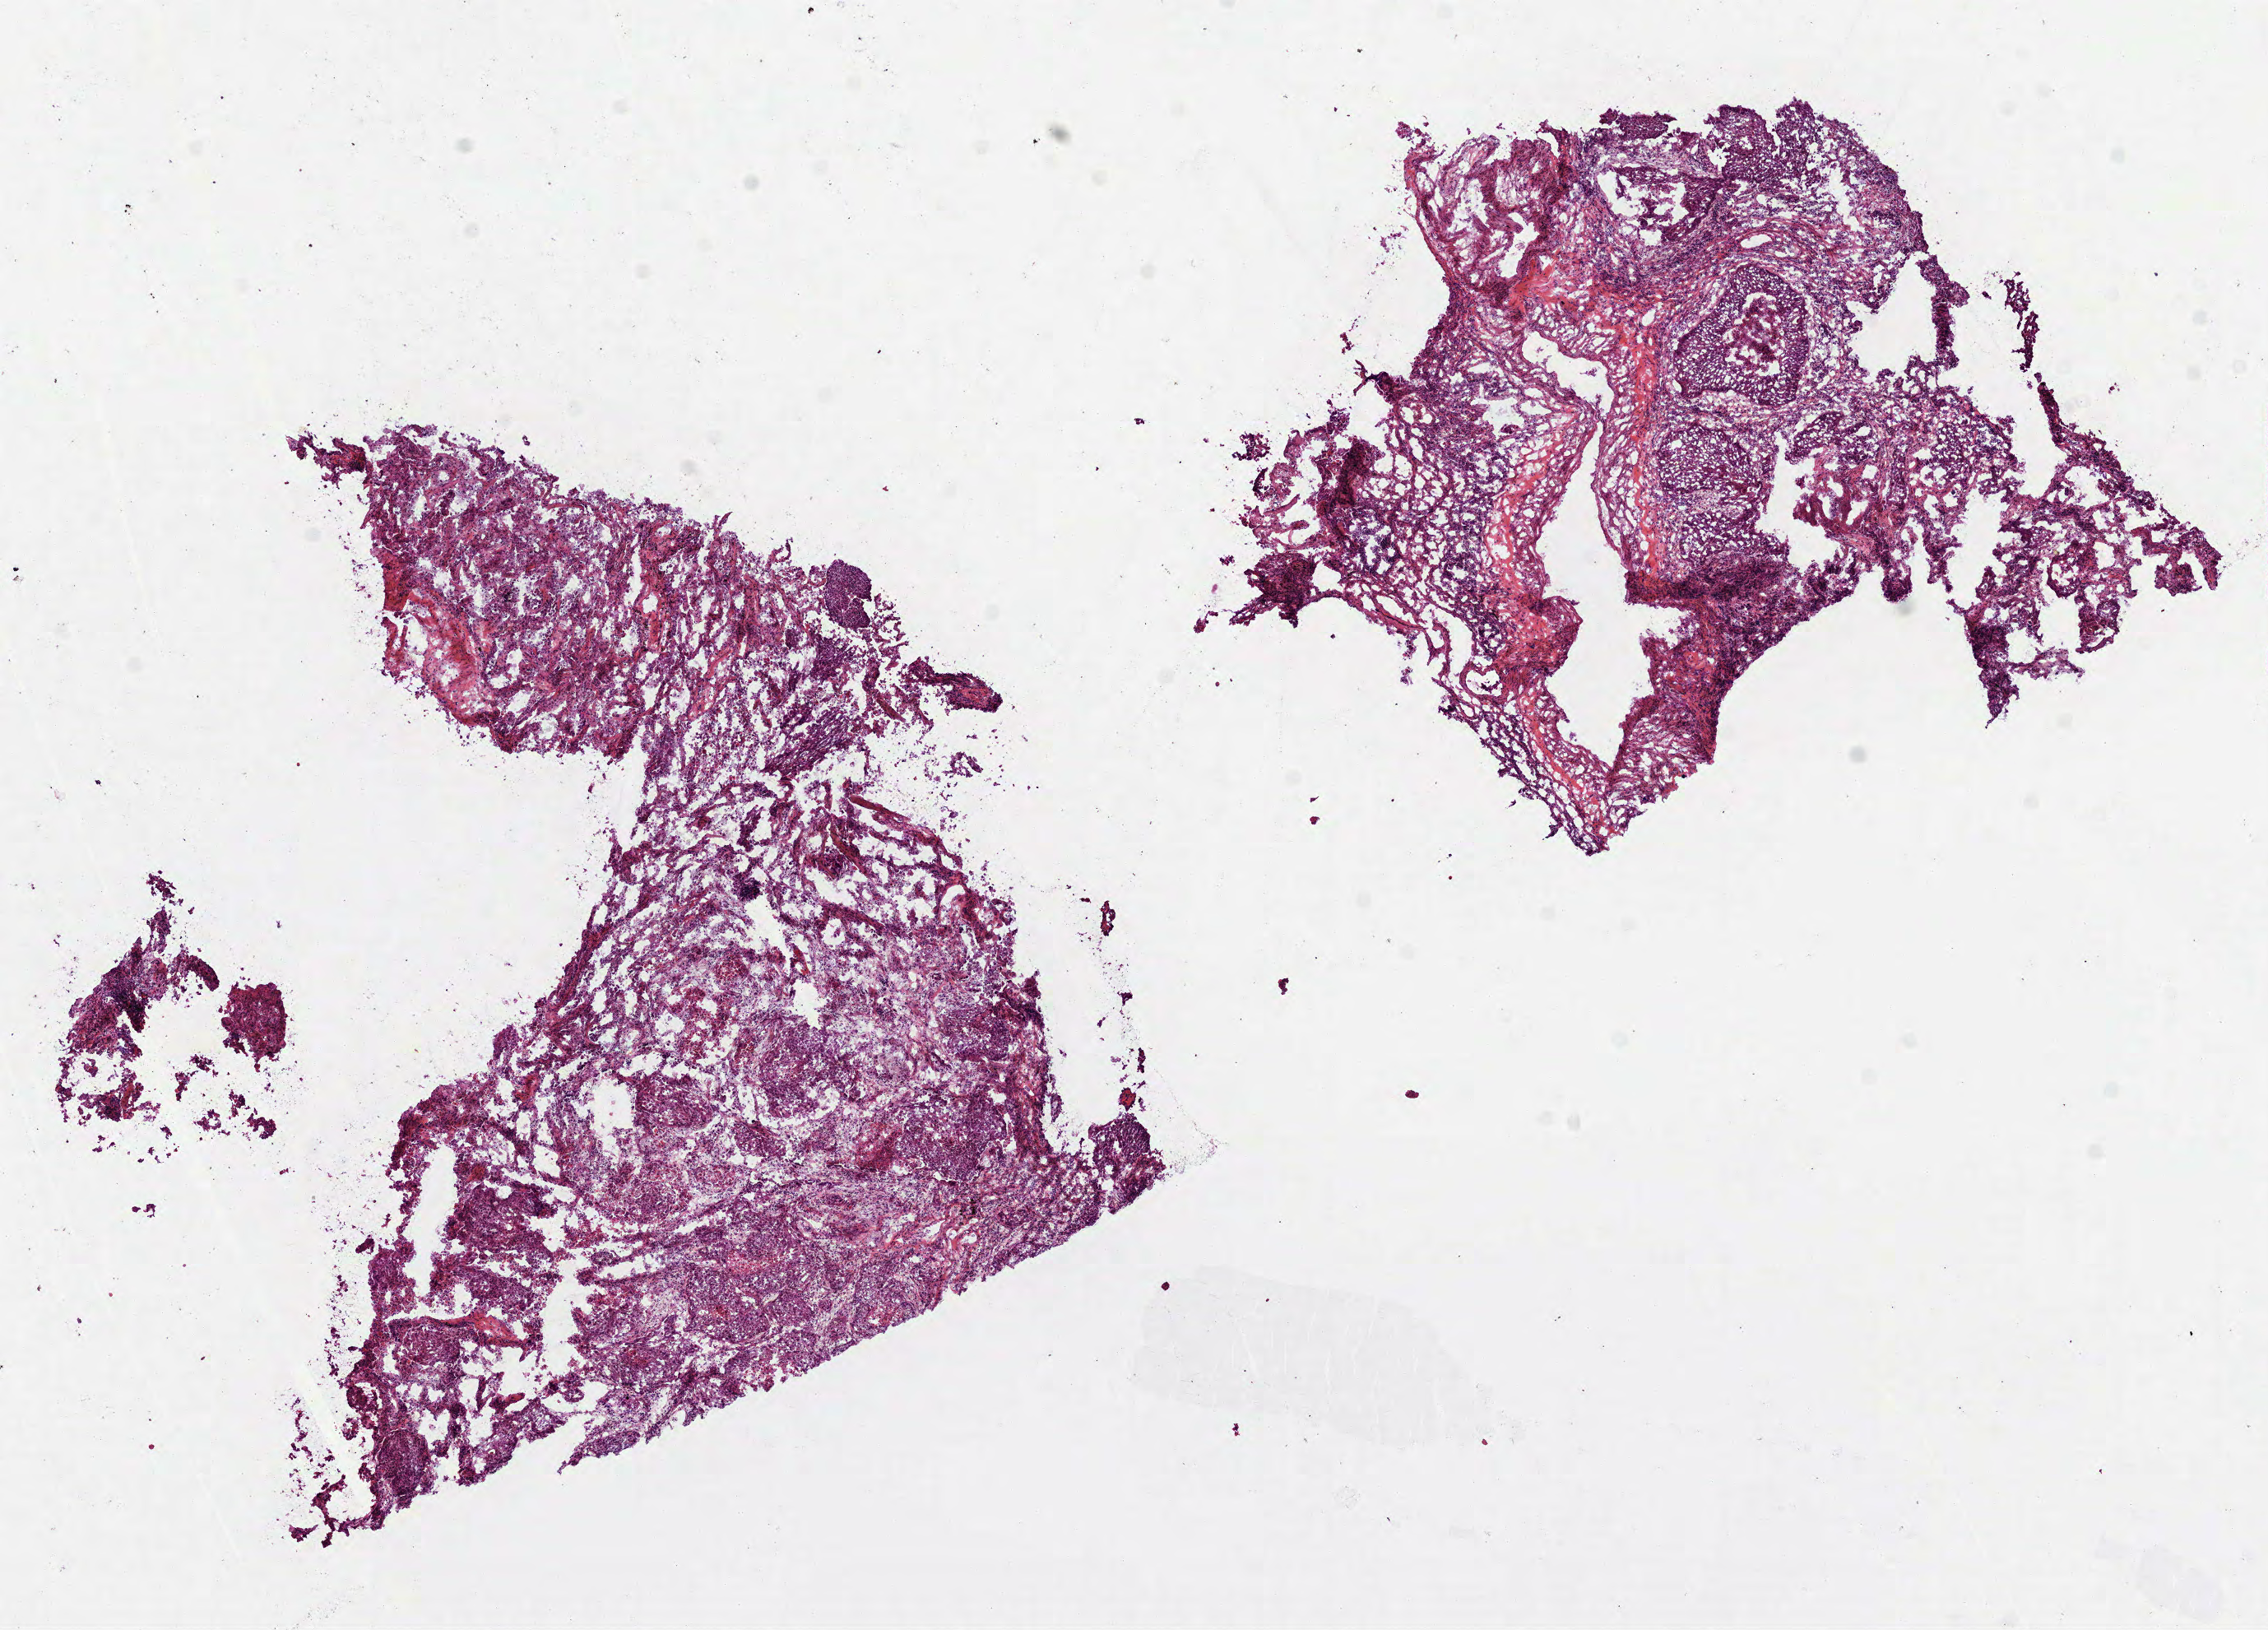
Hematoxylin and eosin (H&E) stained whole-slide image — a low-resolution overview of the entire scanned area, about 11.1 x 8.0 mm (slide scanned at 40x); frozen section from the bottom of the tissue portion; primary tumour sample from the lung. Patient: male, age at initial diagnosis 73 years. Composition of this section per pathologist review: tumour cells 68%, tumour nuclei 60%, normal cells 32%, stromal cells 0%, necrosis 0%.
- histologic diagnosis: Squamous cell carcinoma, NOS (lower lobe, lung)
- AJCC pathologic stage: IB (7th edition)